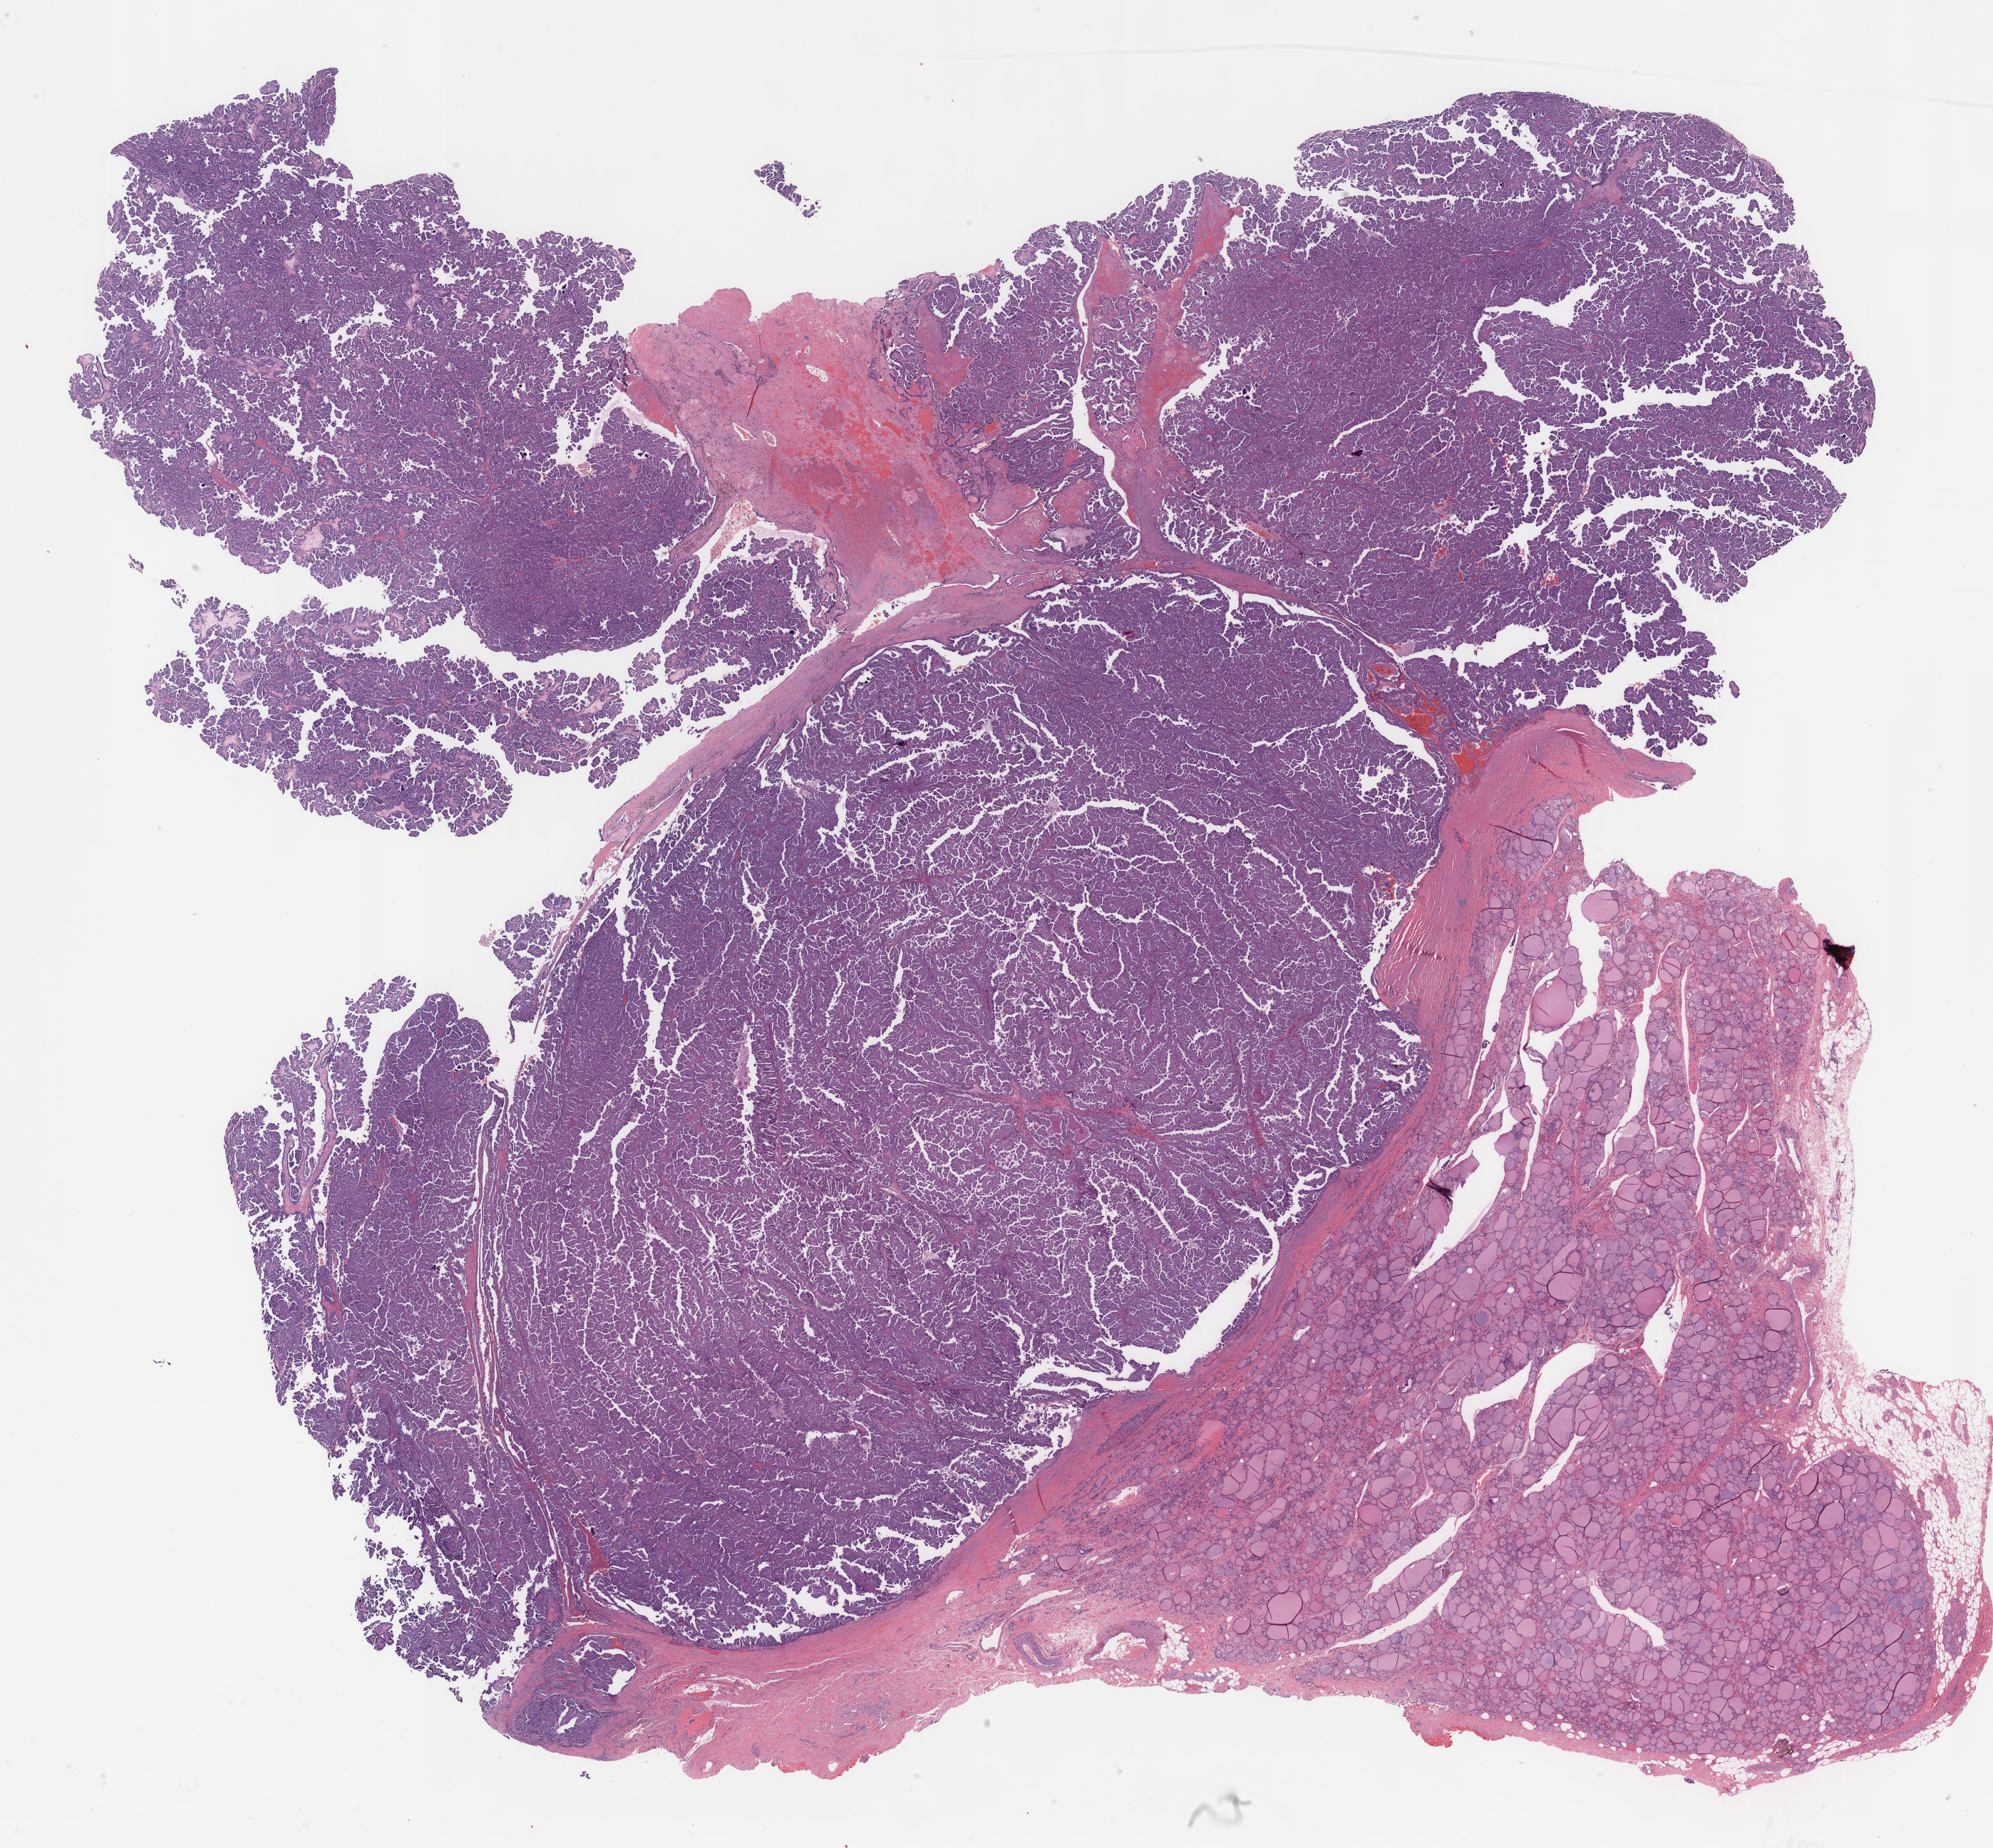
Digitized H&E tissue section (whole slide) — low-resolution overview of the scanned area, about 22.2 x 20.6 mm (acquisition: 40x scan); formalin-fixed paraffin-embedded (FFPE) diagnostic section; thyroid, primary tumour sample. Male, age 70 years at initial diagnosis.
Lymph nodes positive (case pathology): 7 of 15 examined. TNM: T3 N1a M0. AJCC pathologic stage: III. Diagnosis: Papillary adenocarcinoma, NOS (thyroid gland).